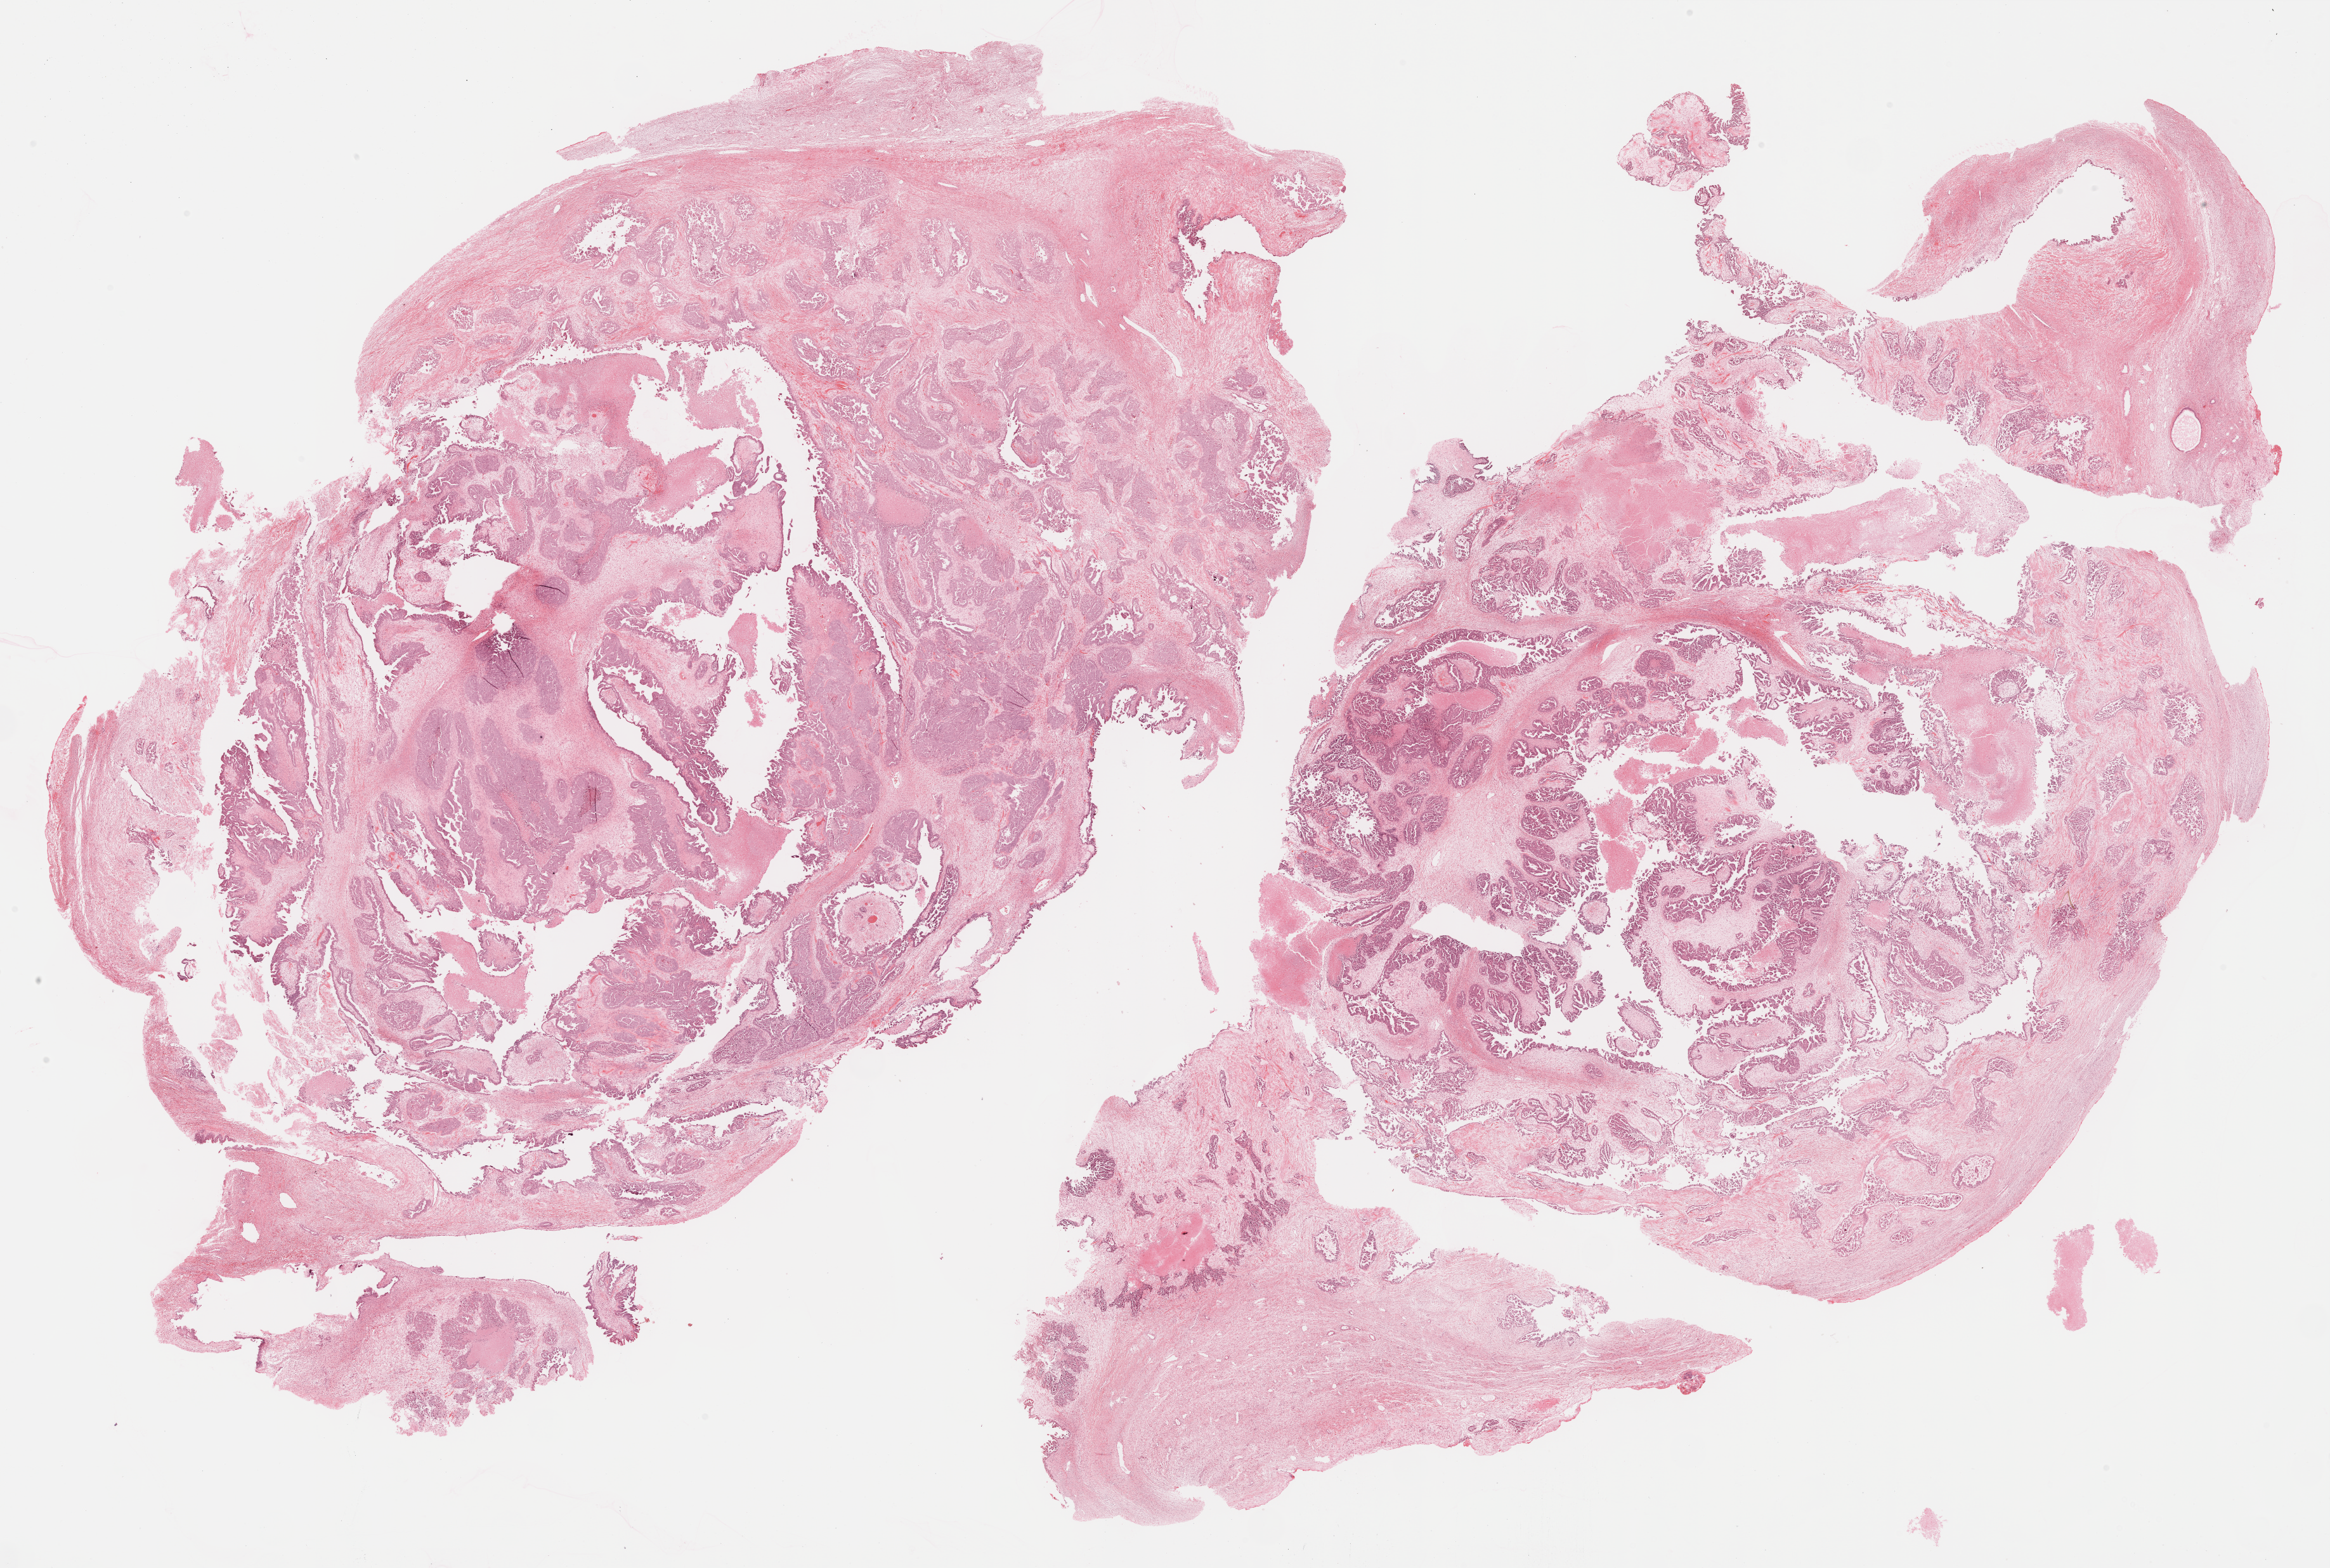
Whole-slide histology image, Hematoxylin and eosin (H&E) stained, shown as a low-resolution overview of the whole scanned area (about 29.7 x 20.0 mm), formalin-fixed paraffin-embedded (FFPE) diagnostic section, primary tumour sample from the ovary. Female, age 72 years at initial diagnosis. Histologic grade: G3 (poorly differentiated).
- laterality: bilateral
- diagnosis: Serous cystadenocarcinoma, NOS
- FIGO stage: IIIC